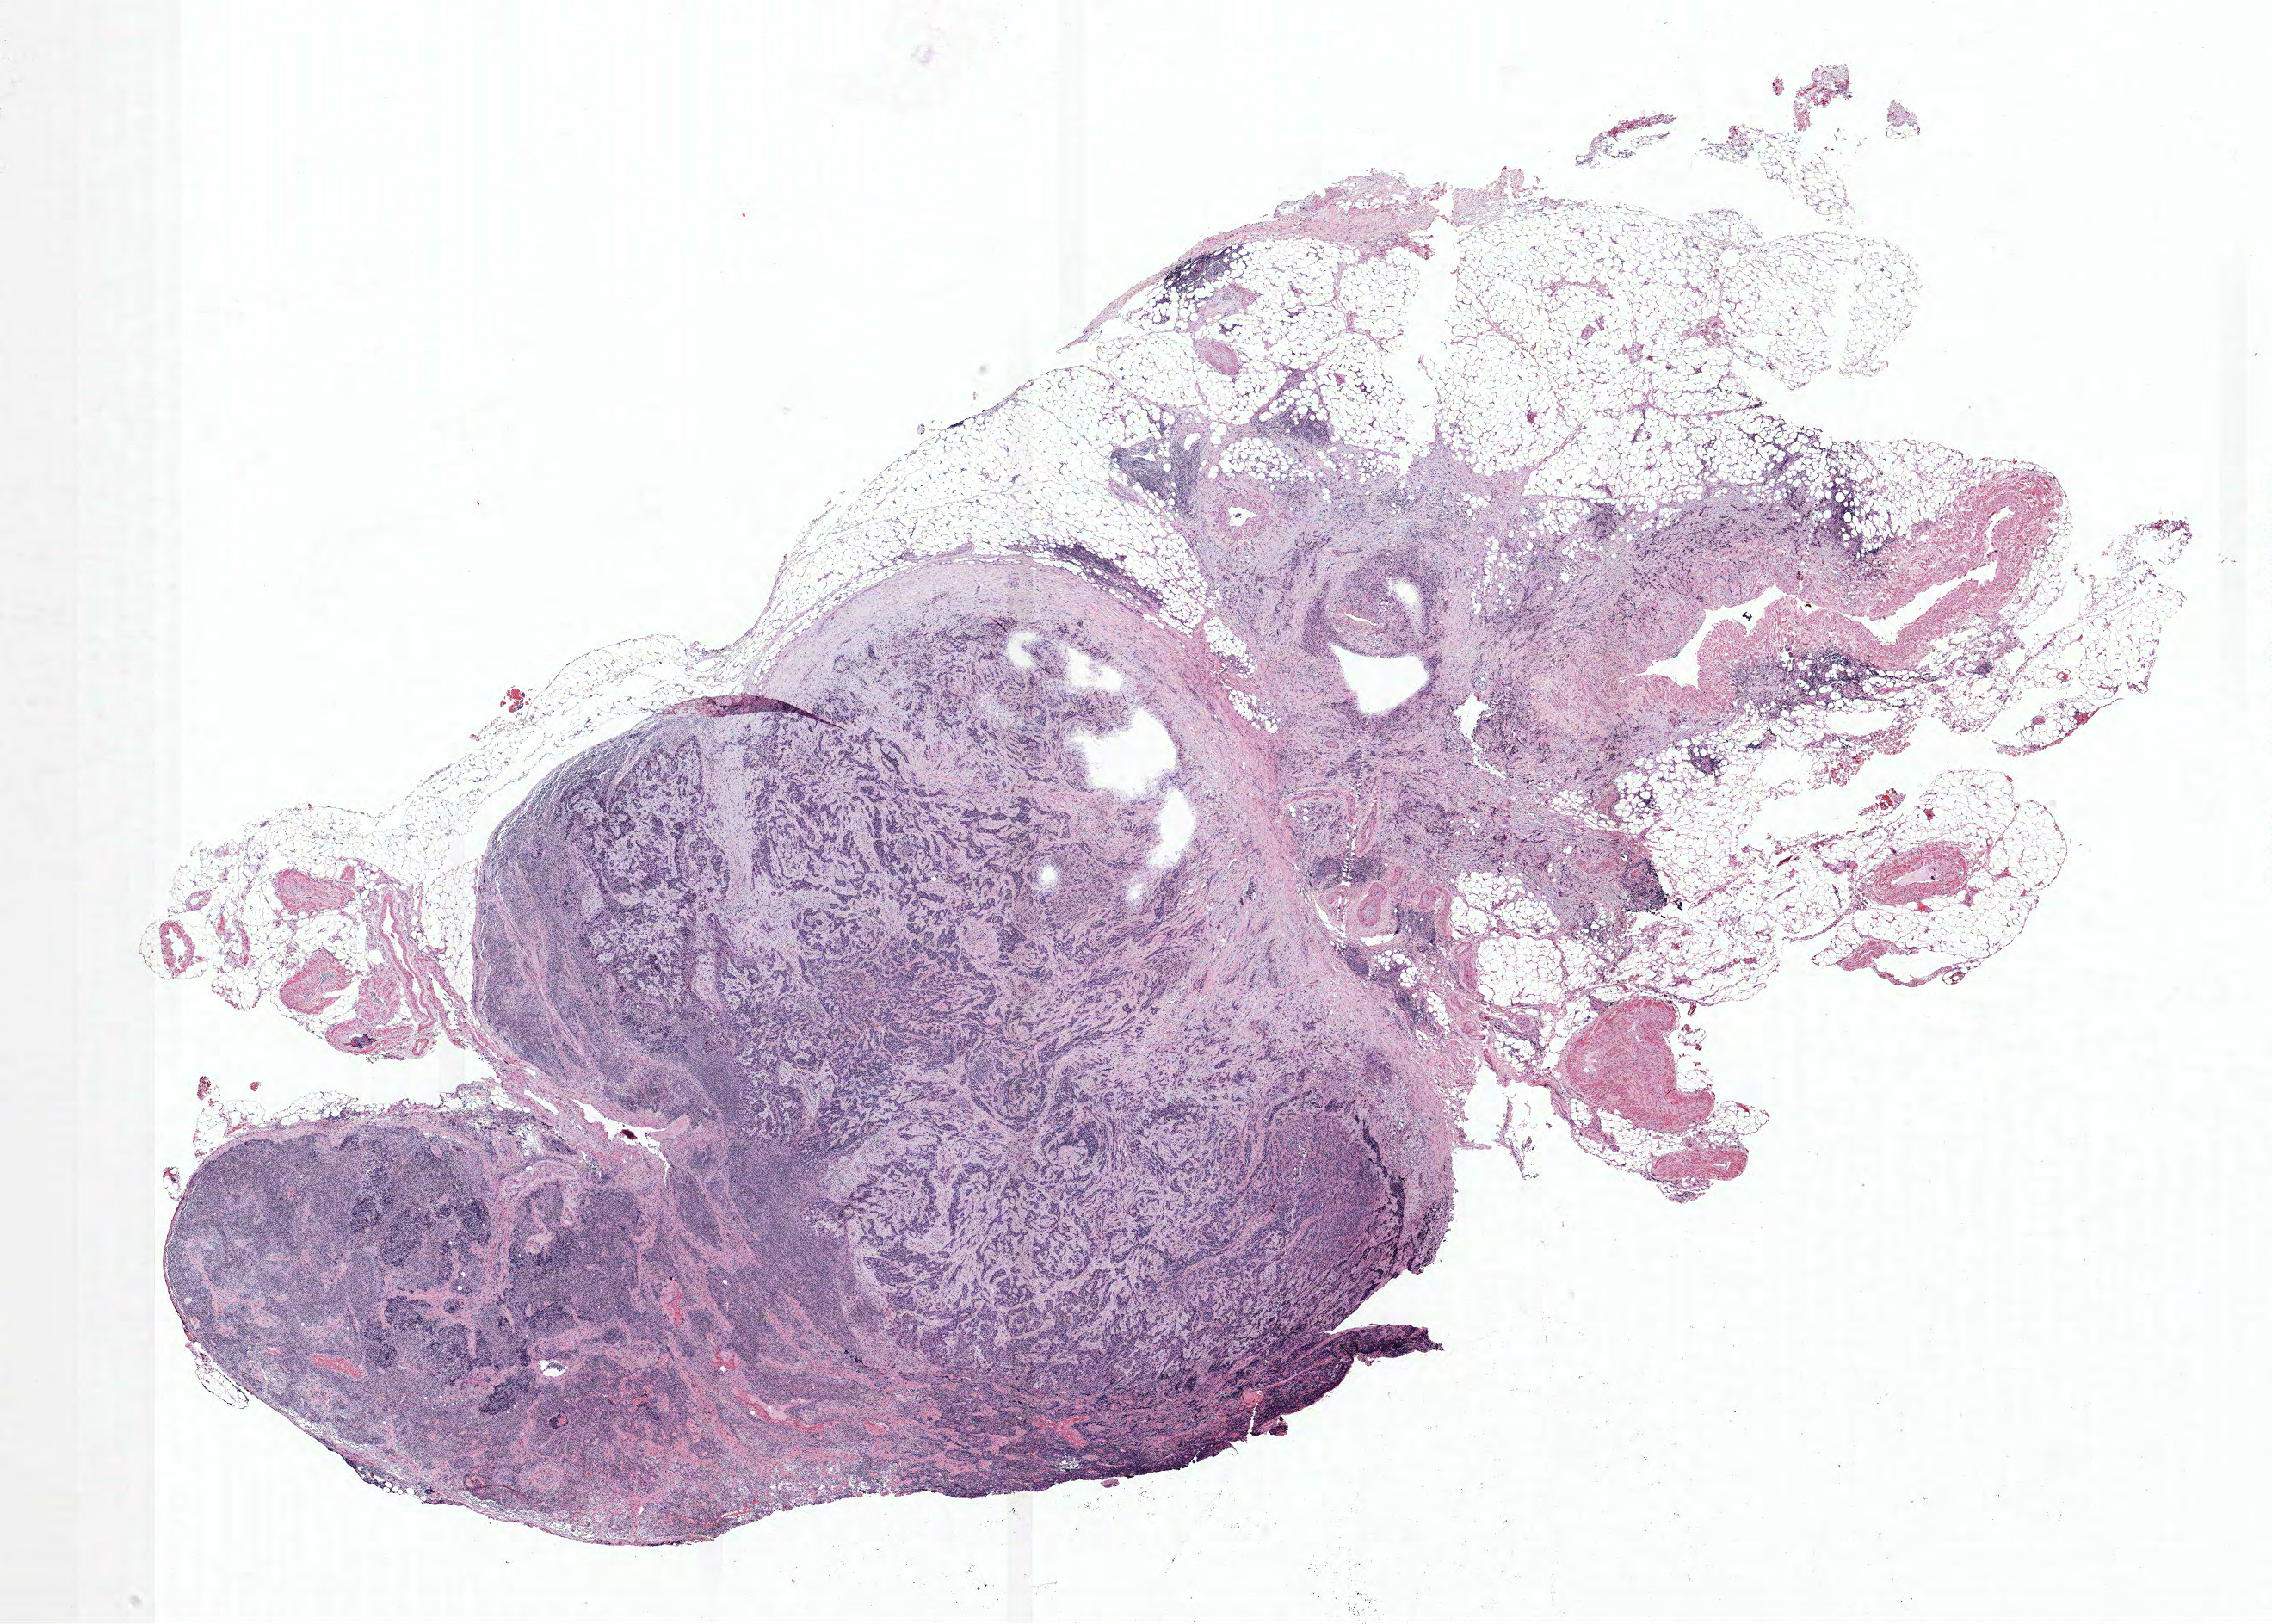
Whole-slide histology image, H&E-stained — a low-resolution overview of the entire scanned area, about 21.1 x 15.1 mm (acquisition: 40x scan), FFPE section, lung. Male patient, aged 62 at enrolment. Former smoker at enrolment. Grade: poorly differentiated (G3).
* stage (AJCC 6th edition): IV
* tumour size (pathology): 15 mm
* participant's lung-cancer diagnosis: Adenocarcinoma, NOS (ICD-O-3 8140/3)
* primary tumour location (clinical record): right lower lobe